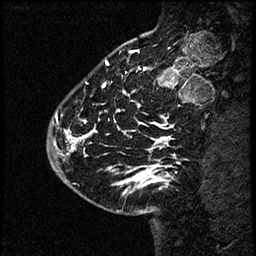
Breast MRI (dynamic contrast-enhanced), one sagittal slice. Position 17 of 60 along the scan axis. Dynamic contrast-enhanced study with each time point stored as its own series, time point 2 of 4 at this slice position (early post-contrast, ordered by acquisition time). 1.5 T. TE 4.2 ms, TR 17.6 ms. 2 mm slice thickness. 256 × 256 image matrix. Female patient, age 43 years. Case-level facts recorded for this patient, not image findings: setting: breast cancer imaged before/during neoadjuvant chemotherapy.
Annotated regions visible in this slice (semi-automatically segmented with operator editing):
- analysis volume of interest (the breast-tissue region the enhancement analysis was run in; not a lesion): bounding box <52,56,169,191> (left, top, right, bottom; pixels)
- tumour enhancement mask (voxels above the 100 % enhancement threshold inside the analysis volume of interest): <54,82,169,183>